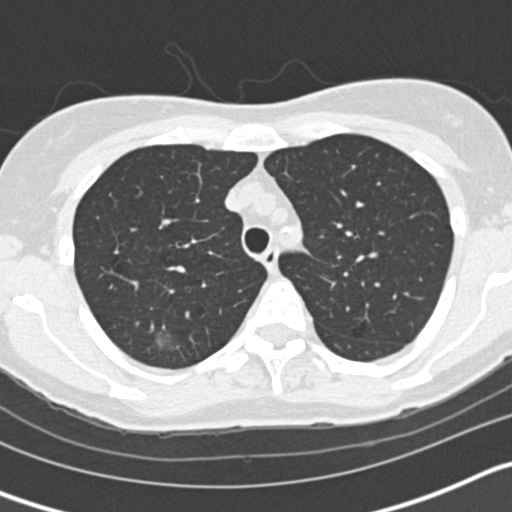
Axial slice from a low-dose chest CT screening exam; second screening round (one year after baseline); lung window (W 1500 / L -600 HU); 2 mm slice thickness; standard (soft-tissue) reconstruction kernel (B30f); 120 kVp. Female participant, aged 58 years at enrolment.
Expert-annotated lung lesion, bounding box (x1, y1, x2, y2) in pixels: (133, 320, 191, 365). The screening reader recorded 3 non-calcified nodules or masses ≥4 mm on this exam; which of them this box marks is not recorded. Official screen result: positive, other. Participant outcome: lung cancer diagnosed 59 days after this screen — bronchiolo-alveolar adenocarcinoma, NOS, right upper lobe, moderately differentiated (G2), stage IA (AJCC 6th edition), 7 mm at pathology.